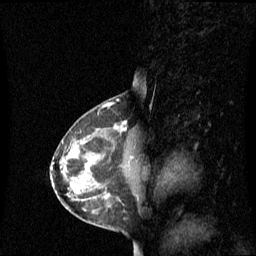
Breast MRI (dynamic contrast-enhanced), one sagittal slice; position 35 of 60 along the scan axis; dynamic contrast-enhanced series, image 2 of 3 at this slice position (ordered by acquisition); 1.5 T; TE 4.2 ms, TR 8.4 ms; 2.1 mm slice thickness; 256 × 256 image matrix, field of view 240 × 240 mm. Female patient, age 42 years. Case-level facts recorded for this patient, not image findings: setting: breast cancer imaged before/during neoadjuvant chemotherapy; receptor status: HR-positive, HER2-negative.
Structures marked on this image (semi-automatically segmented with operator editing):
- analysis volume of interest (the breast-tissue region the enhancement analysis was run in; not a lesion): bounding box (x1, y1, x2, y2) in pixels: (78, 122, 135, 195)
- tumour enhancement mask (voxels above the 70 % enhancement threshold inside the analysis volume of interest): (86, 128, 119, 165)